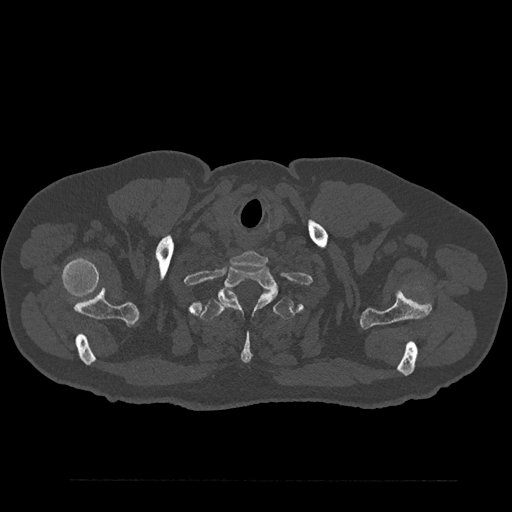
CT including the spine, one axial slice; position 743 of 797 along the scan axis; 120 kVp; bone window (W 1800 / L 400 HU); 512 × 512 image matrix, field of view 430 × 430 mm. Male patient, age 61 years. Case-level facts recorded for this patient, not image findings: primary cancer: prostate.
Outlined on this slice (semi-automatic segmentation, software-assisted and operator-edited):
- T1 vertebra: bounding box [x1, y1, x2, y2] px = [218, 267, 277, 309]
- T2 vertebra: [200, 290, 295, 364]